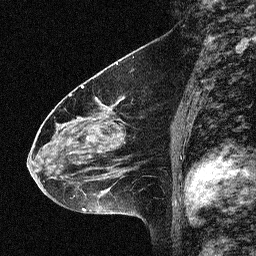
Breast MRI (dynamic contrast-enhanced), one sagittal slice; position 33 of 64 along the scan axis; dynamic contrast-enhanced study with each time point stored as its own series, time point 2 of 3 at this slice position (early post-contrast, ordered by acquisition time); 1.5 T; TE 4.5 ms, TR 11 ms; 2.06 mm slice thickness; 256 × 256 image matrix, field of view 200 × 200 mm. Patient: female, 46 years. Case-level facts recorded for this patient, not image findings: setting: breast cancer imaged before/during neoadjuvant chemotherapy; receptor status: HER2-positive.
Annotated regions visible in this slice (semi-automatically segmented with operator editing):
- analysis volume of interest (the breast-tissue region the enhancement analysis was run in; not a lesion): box from (x=42, y=80) to (x=150, y=180) px
- tumour enhancement mask (voxels above the 90 % enhancement threshold inside the analysis volume of interest): (x=54, y=86)–(x=120, y=179)